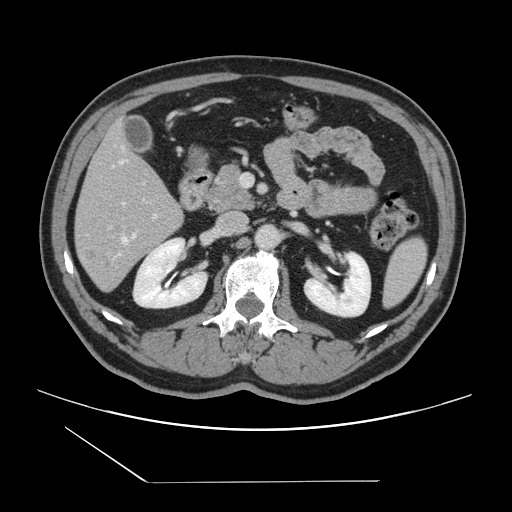
Contrast-enhanced abdominal CT, one axial slice; 120 kVp; intravenous contrast given; soft-tissue window (W 400 / L 40 HU); 2.5 mm slice thickness; 512 × 512 image matrix, field of view 407 × 407 mm. Male patient, age 61 years. Case-level facts recorded for this patient, not image findings: diagnosis: colorectal cancer liver metastases, imaged before liver resection; multiple liver metastases: yes; largest metastasis: 5.5 cm; chemotherapy before resection: no.
Outlined on this slice (outlined manually by an expert reader):
- hepatic veins: bounding box [x1, y1, x2, y2] px = [120, 159, 135, 254]
- liver: [75, 126, 183, 290]
- planned liver remnant (the part of the liver to remain after resection): [77, 125, 173, 218]
- portal vein (with intrahepatic branches): [109, 202, 157, 228]
- liver metastasis: [79, 249, 113, 273]